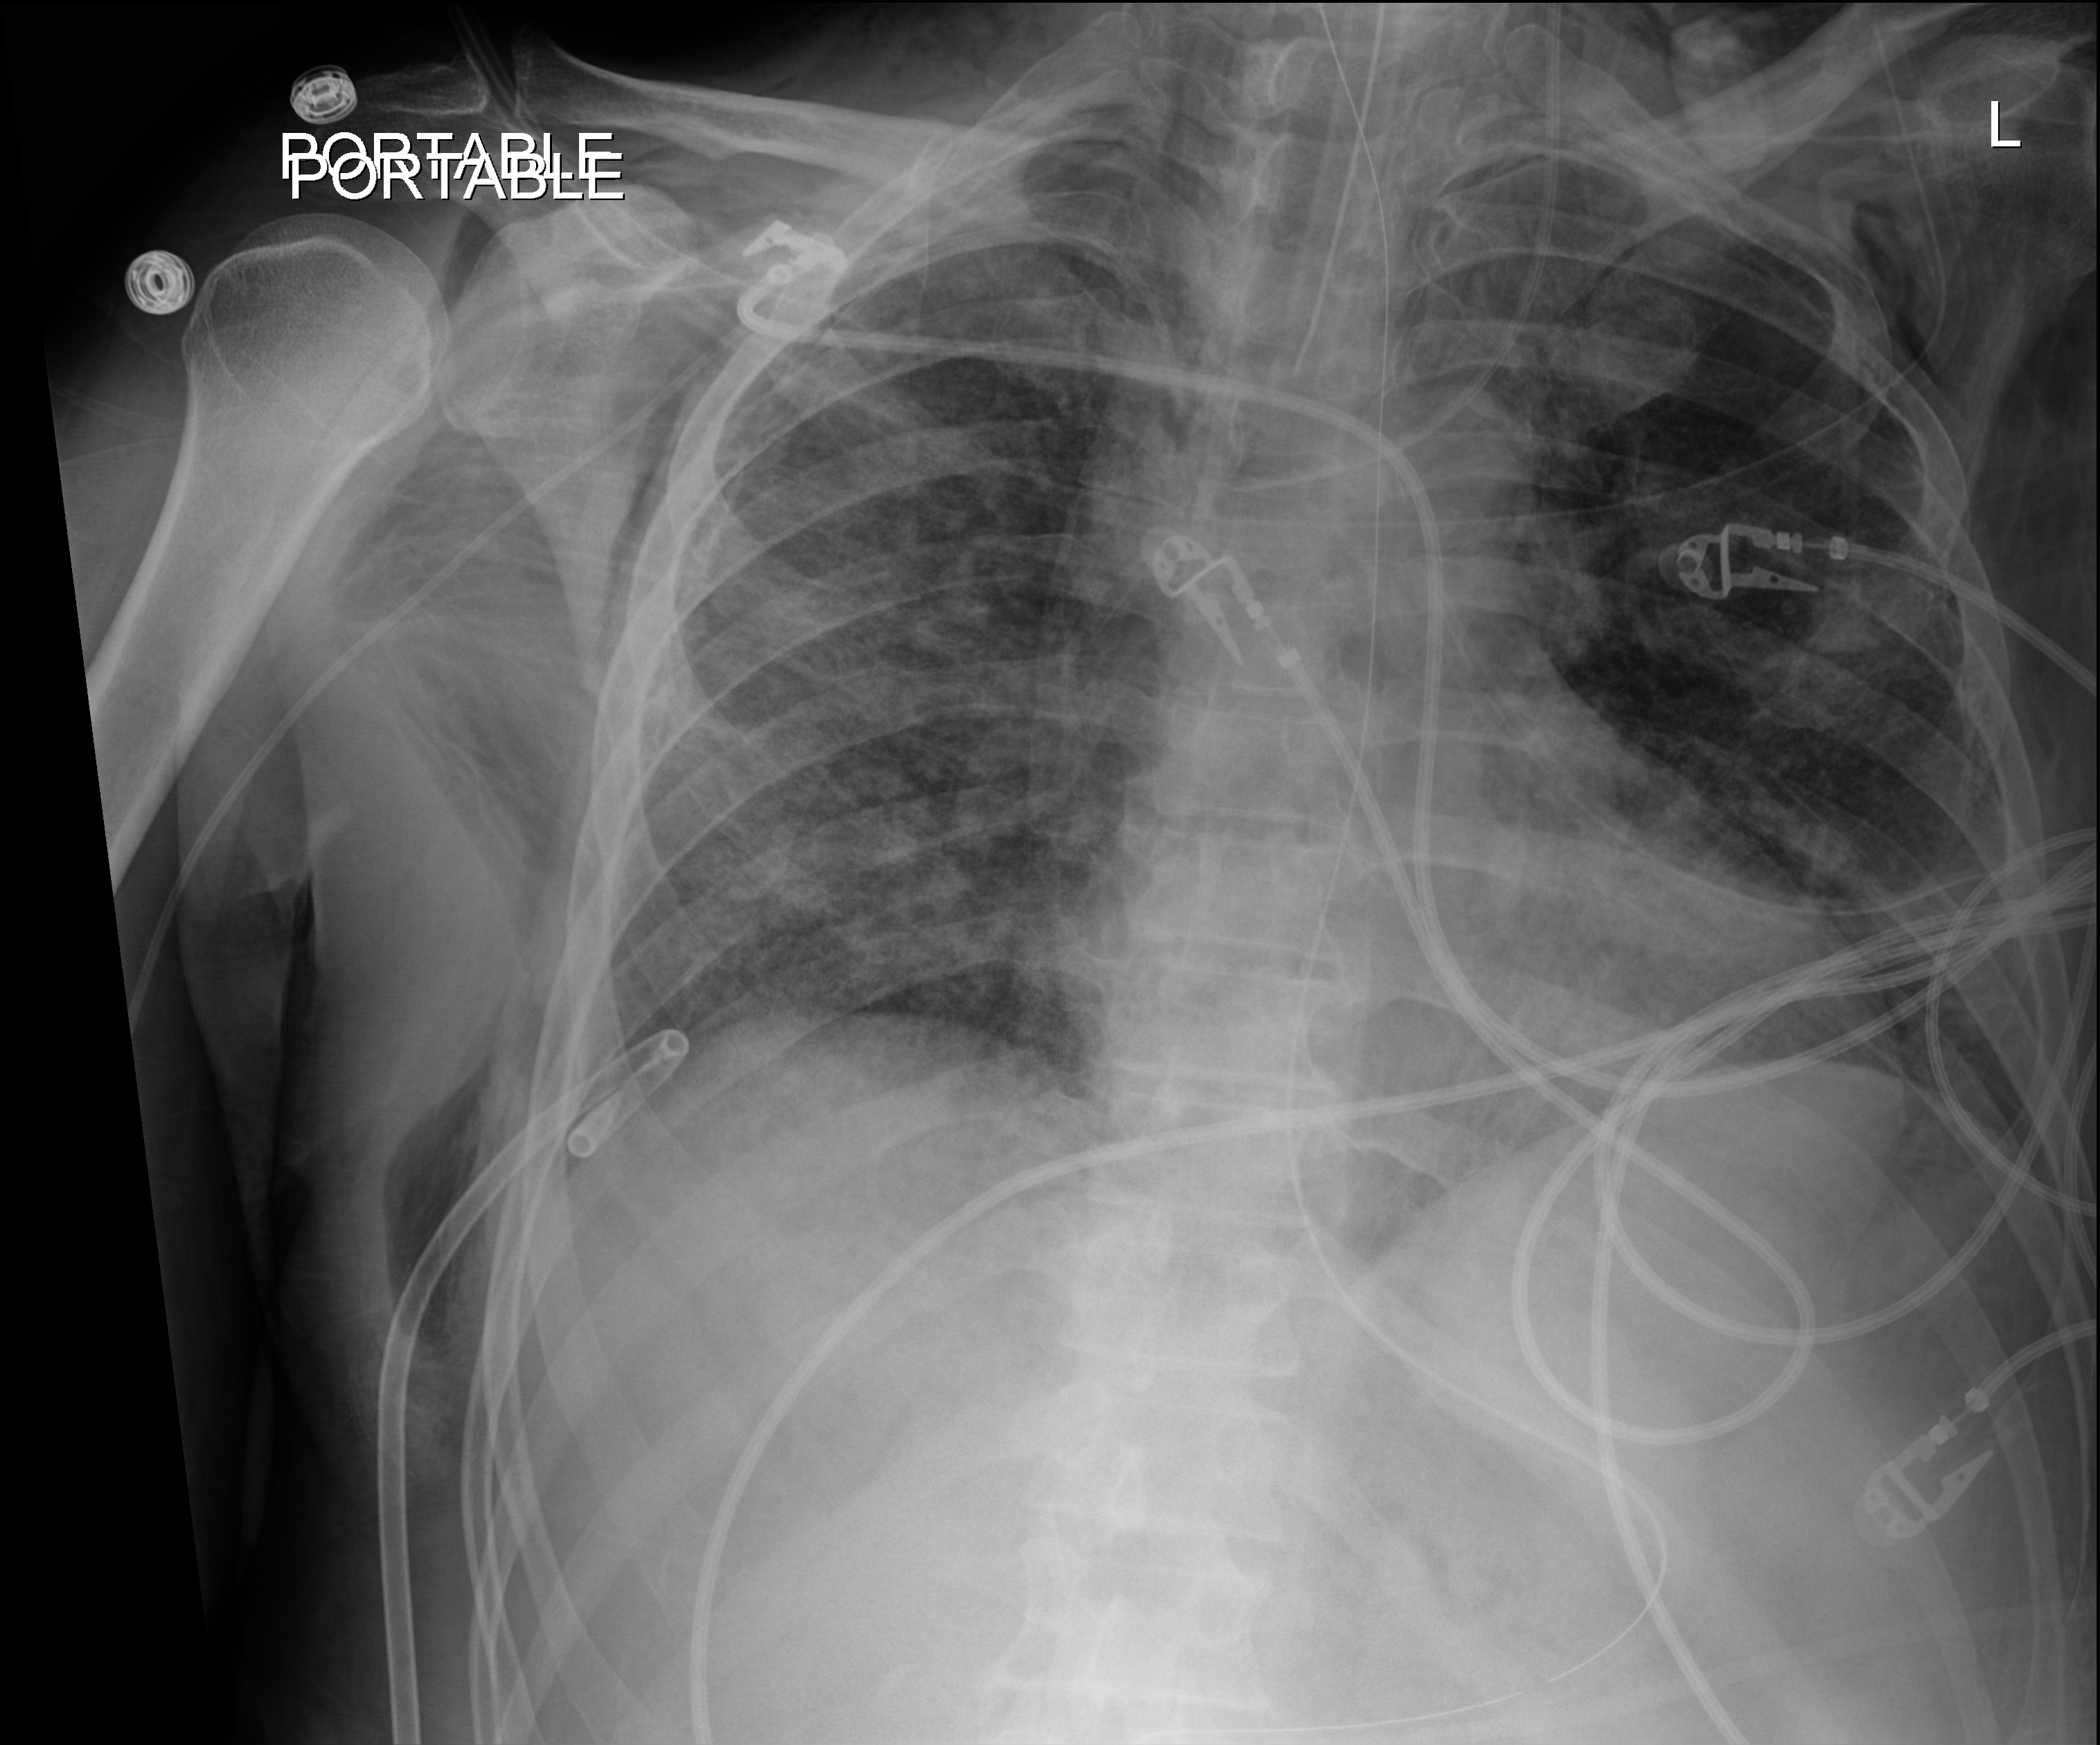
Bedside chest radiograph (digital radiography); anteroposterior (AP) projection. Male patient hospitalised with COVID-19, age 18–59 years.
Admission-level facts for this patient (not findings on this image; timing relative to this image not recorded):
- admitted to intensive care during this hospital stay: yes
- mechanically ventilated during this hospital stay: yes
- smoking status (admission record): never